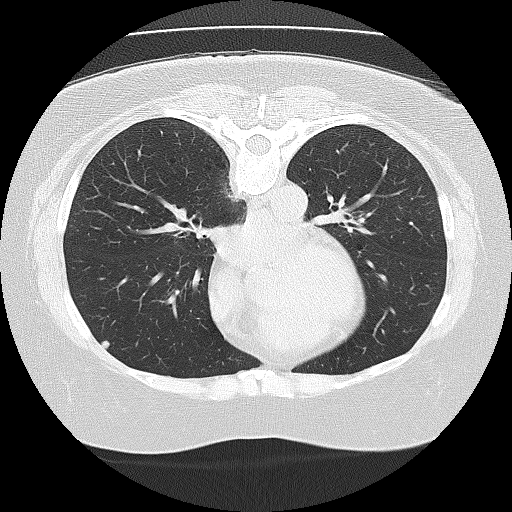
Axial slice from a low-dose chest CT screening exam; second annual screen; lung window (W 1500 / L -600 HU); slice 57 of 103 in the series; 512 × 512 image matrix, field of view 330 × 330 mm. Female participant, aged 67 years at enrolment. Former smoker at enrolment.
Expert-annotated lung lesion, bounding box [x1, y1, x2, y2] px = [82, 325, 127, 366]. The exam's reader record, not a measurement of the box and not confirmed to be the same lesion: non-calcified nodule or mass ≥4 mm, right middle lobe, 5 × 5 mm, smooth margins, soft tissue attenuation, pre-existing on the prior screen: yes; interval growth: no. Official screen result: positive, no significant change: stable abnormalities potentially related to lung cancer, unchanged since the prior screening exam. Lung cancer was diagnosed 247 days after this screen: small cell carcinoma, NOS, right upper lobe, undifferentiated (G4), stage IV (AJCC 6th edition), 60 mm at pathology.